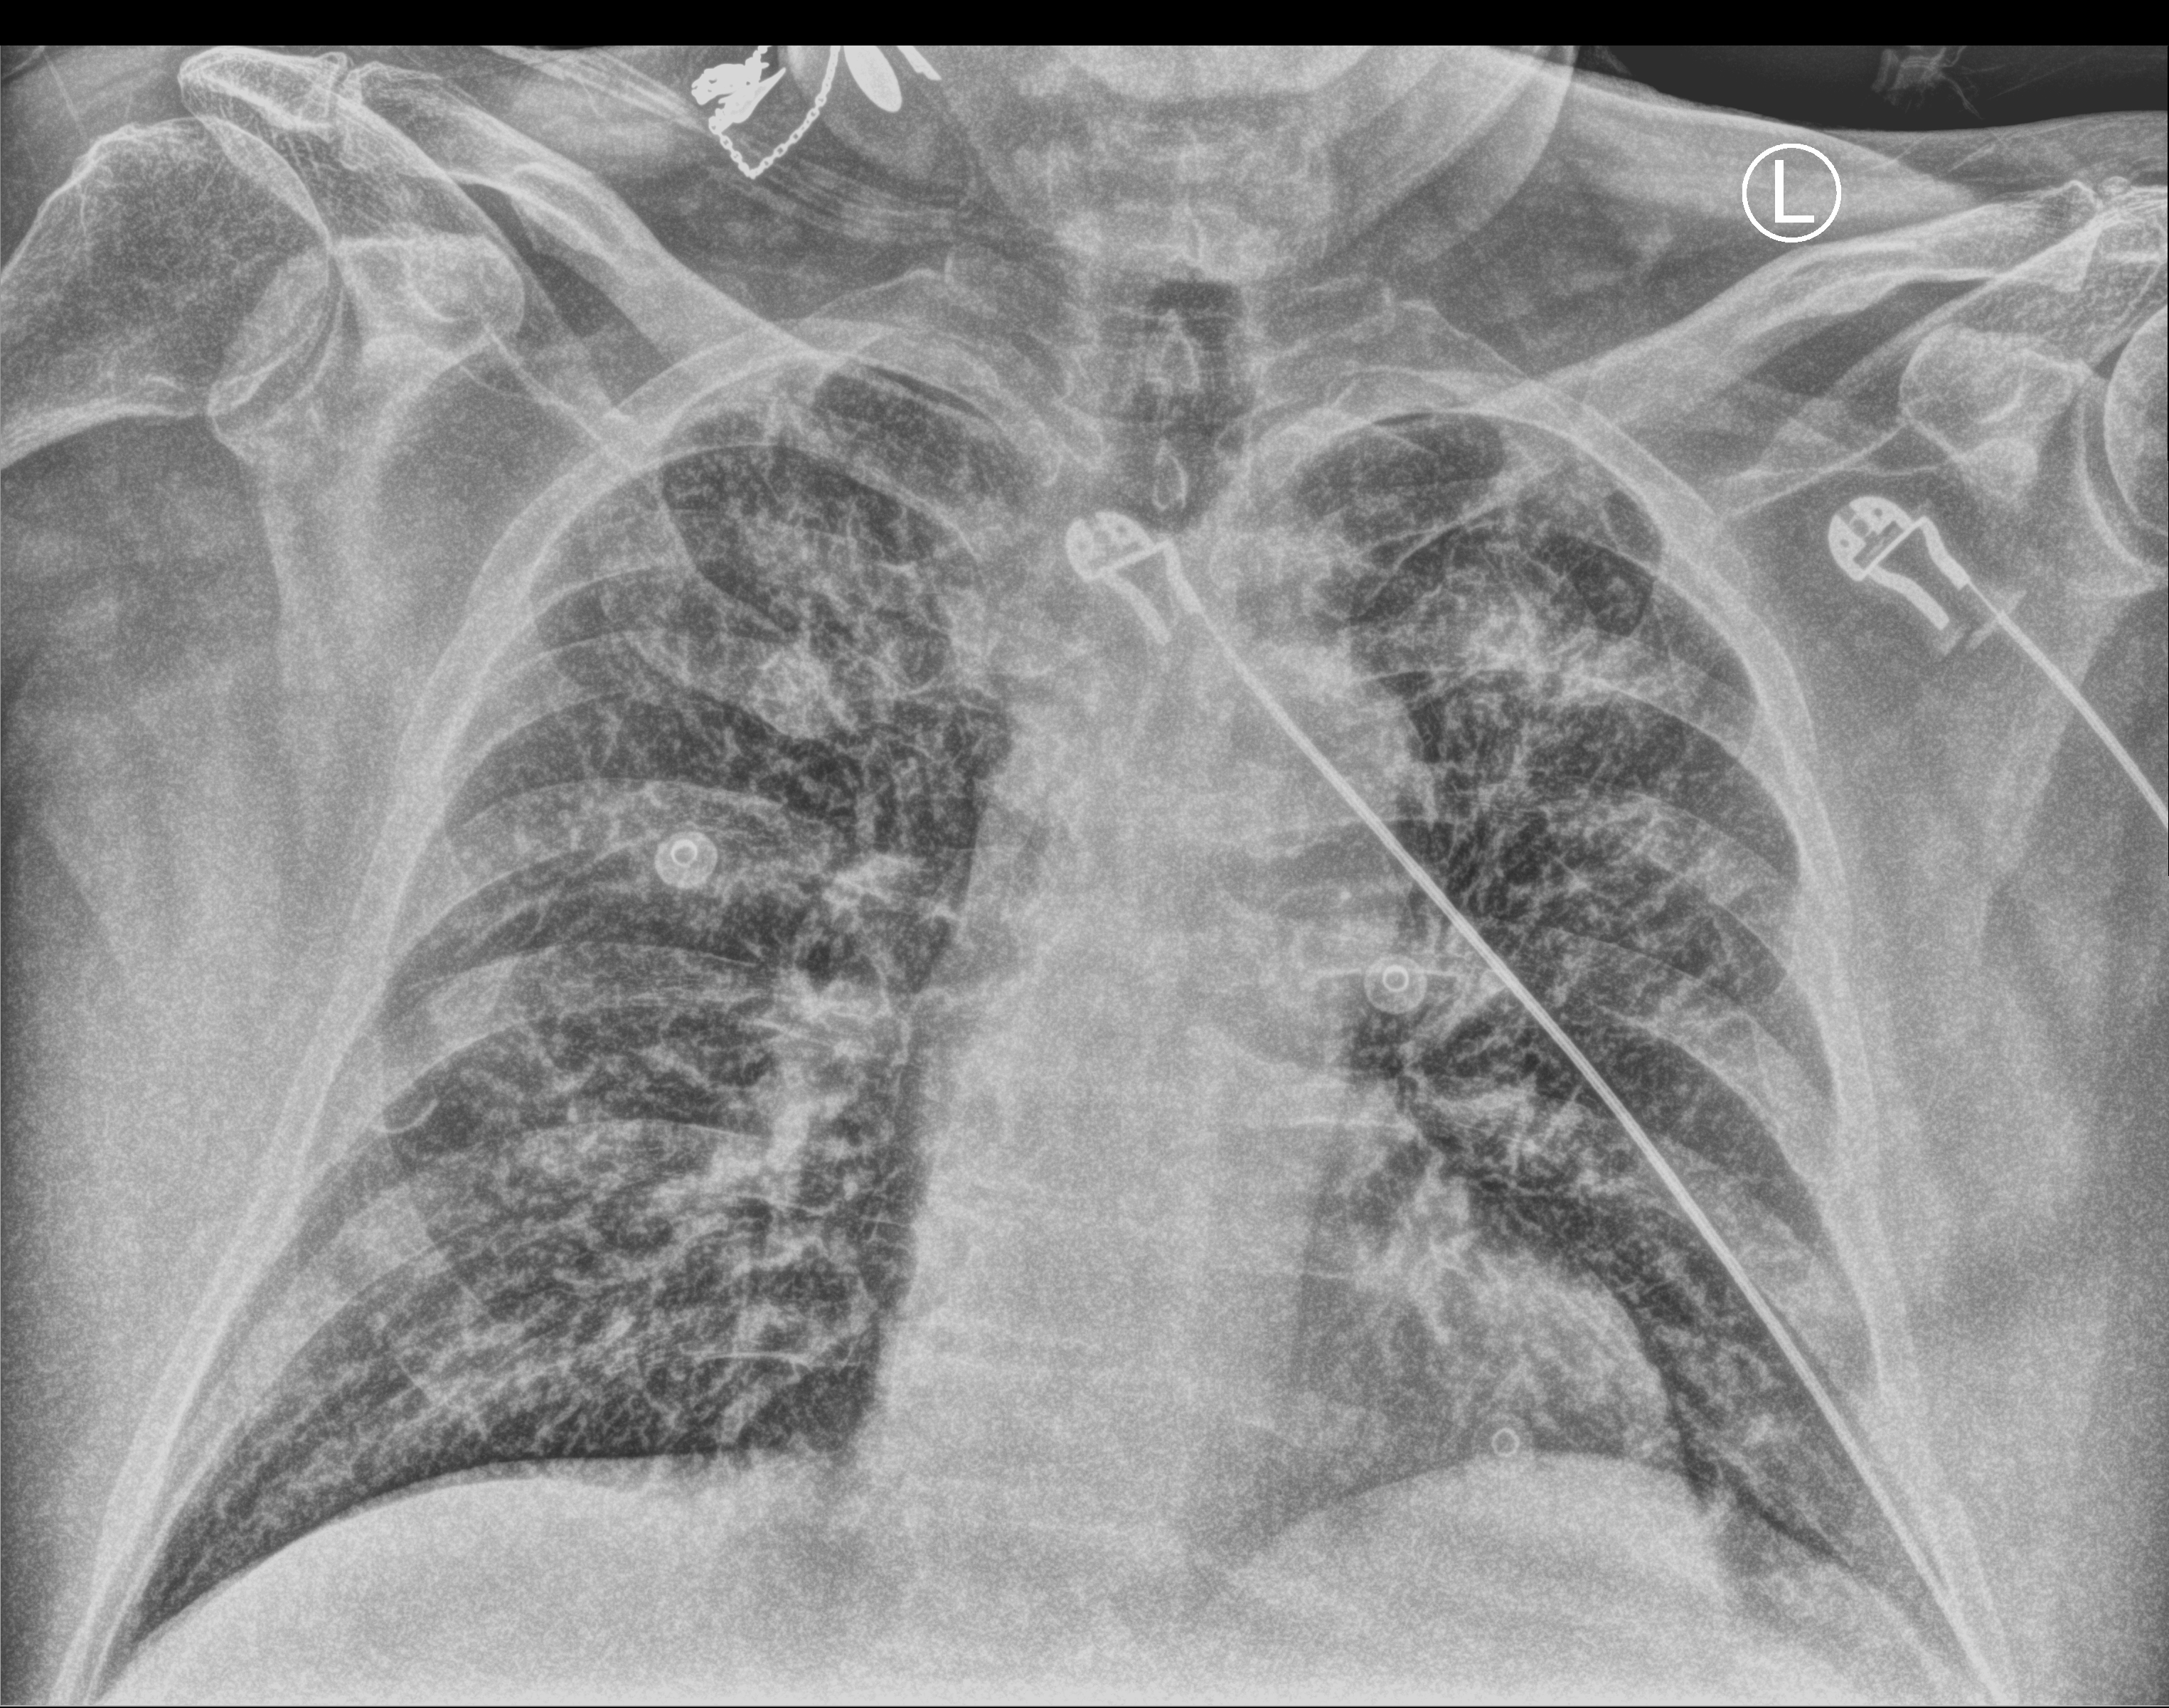
Bedside chest radiograph (computed radiography); anteroposterior (AP) projection. Patient hospitalised with COVID-19; male, aged 75–90 years.
Admission-level facts for this patient (not findings on this image; timing relative to this image not recorded):
- mechanically ventilated during this hospital stay: no
- diabetes (admission record): no